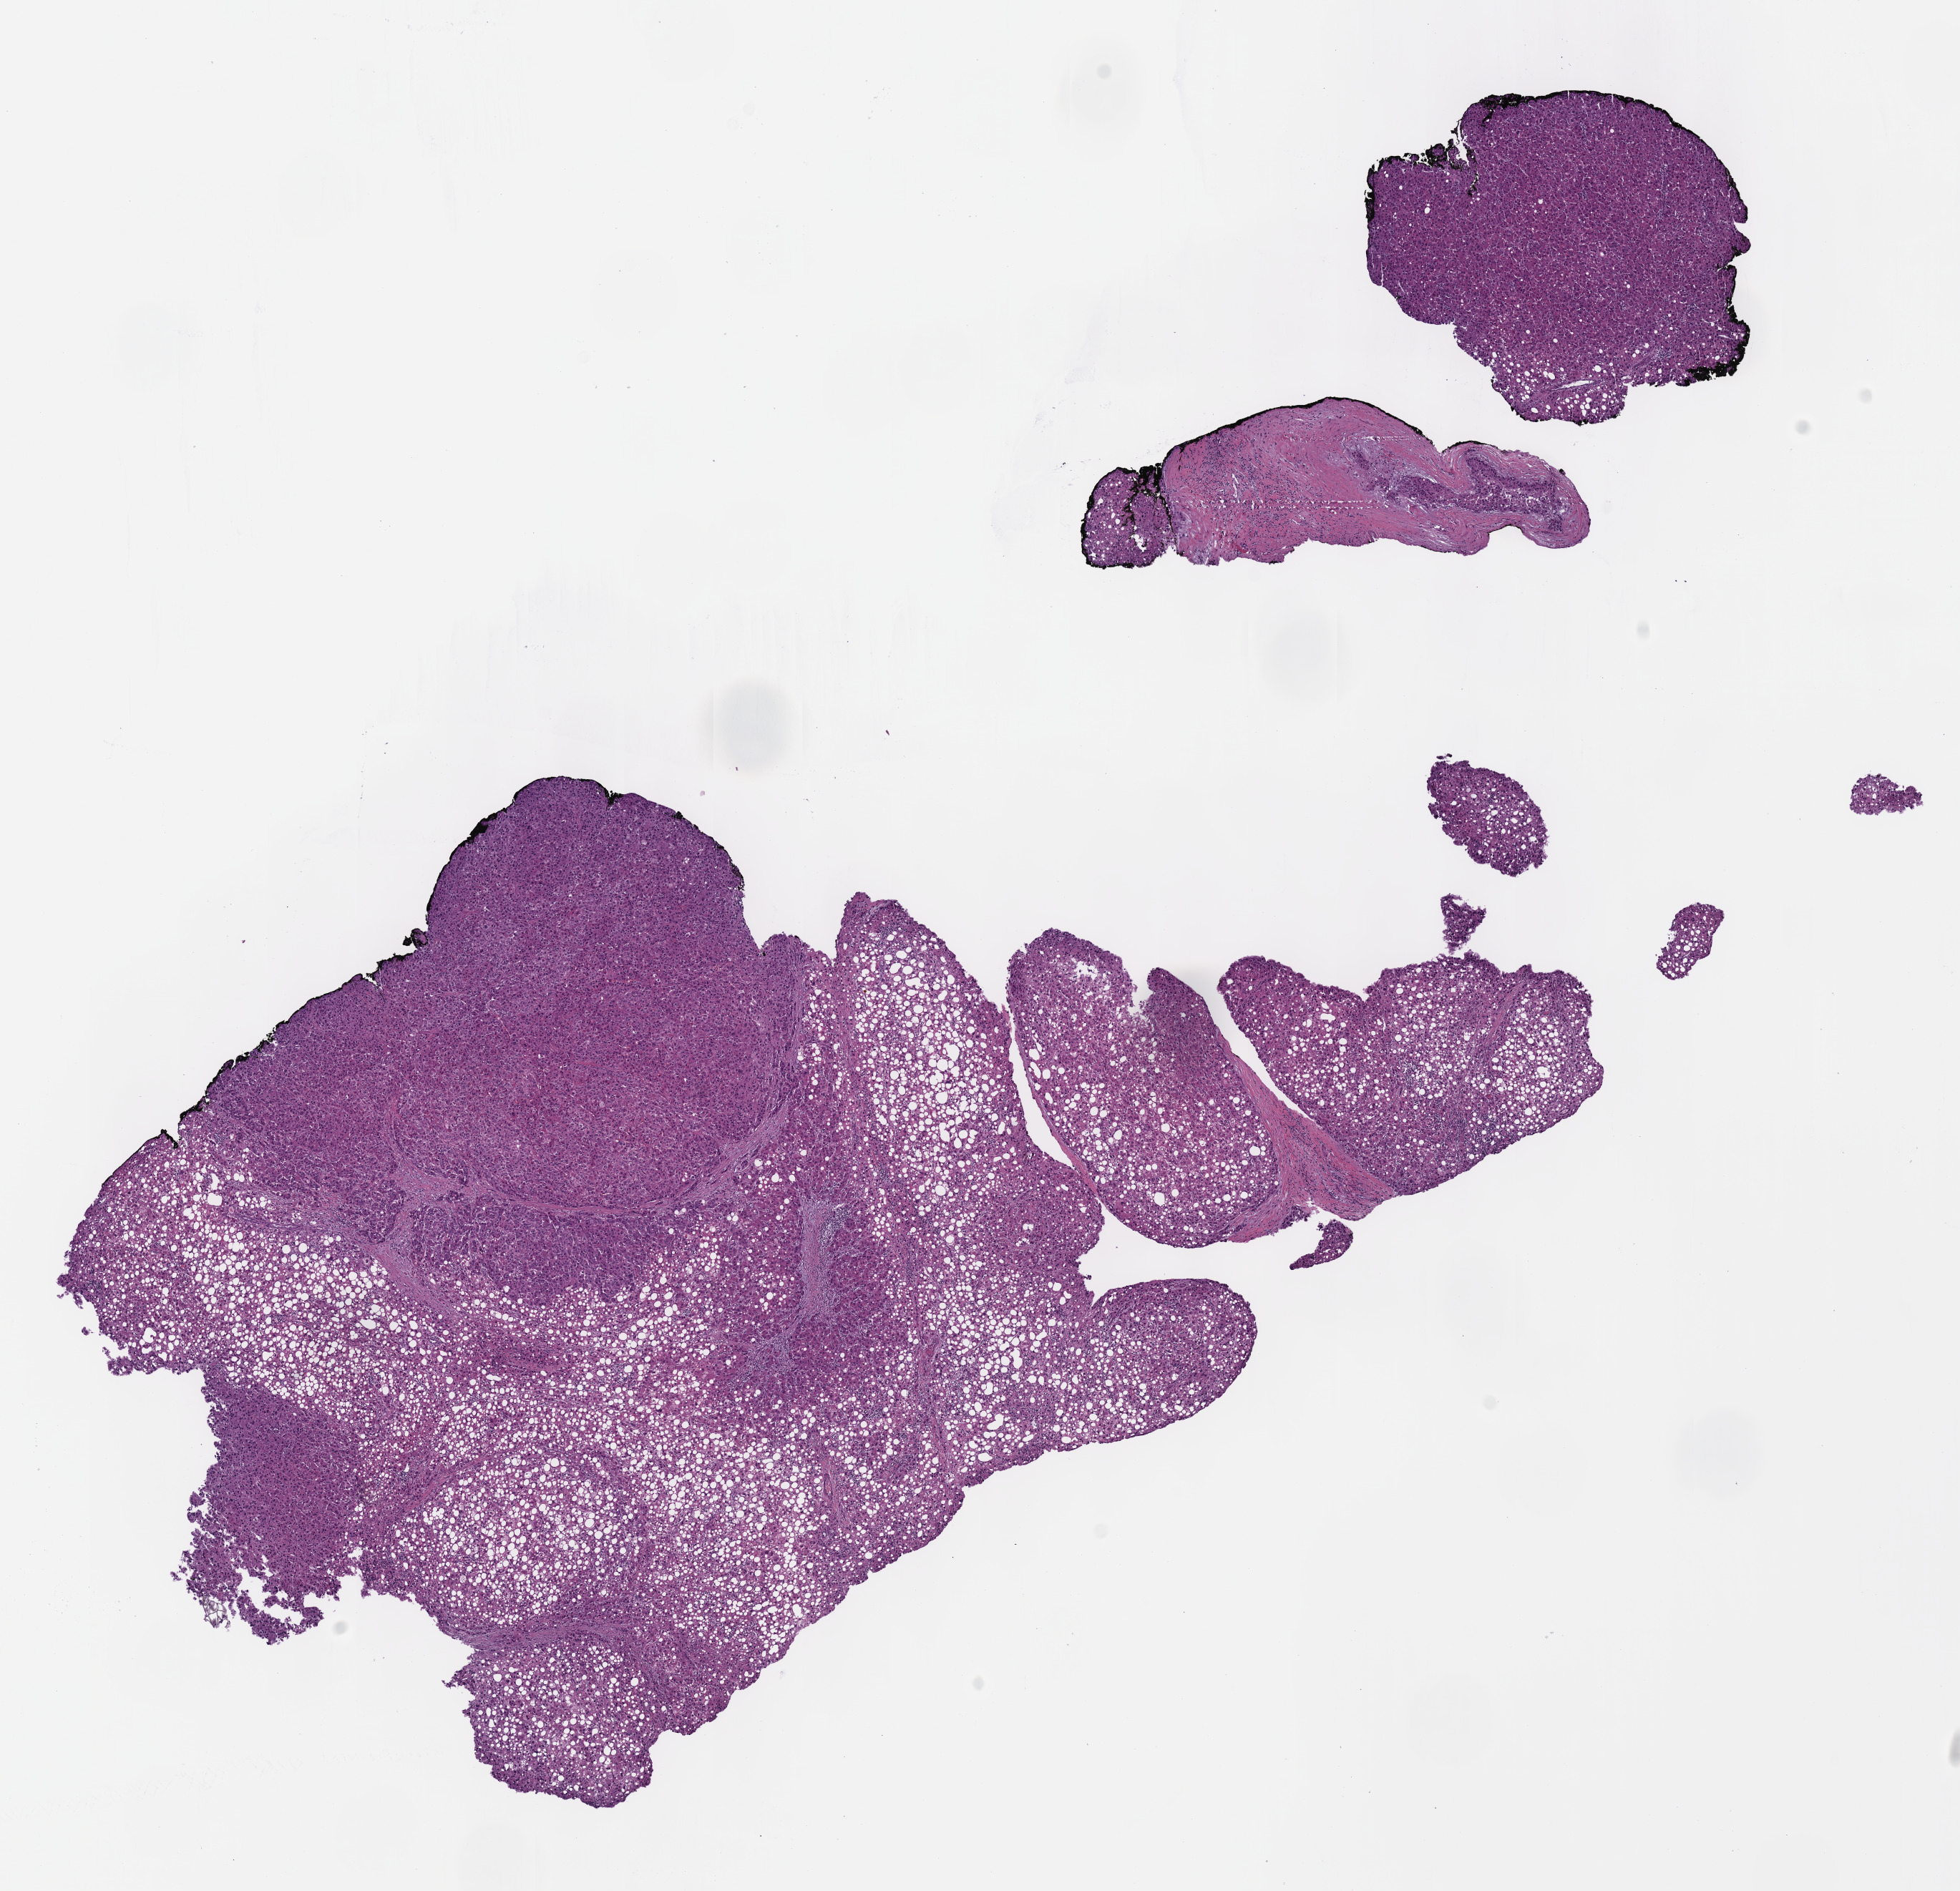
H&E-stained whole-slide image, shown as a low-resolution overview of the whole scanned area (about 10.8 x 10.4 mm, slide scanned at 40x), formalin-fixed paraffin-embedded (FFPE) diagnostic section, liver, primary tumour sample. Male patient; age at initial diagnosis 80 years.
Diagnosis: Hepatocellular carcinoma, NOS.